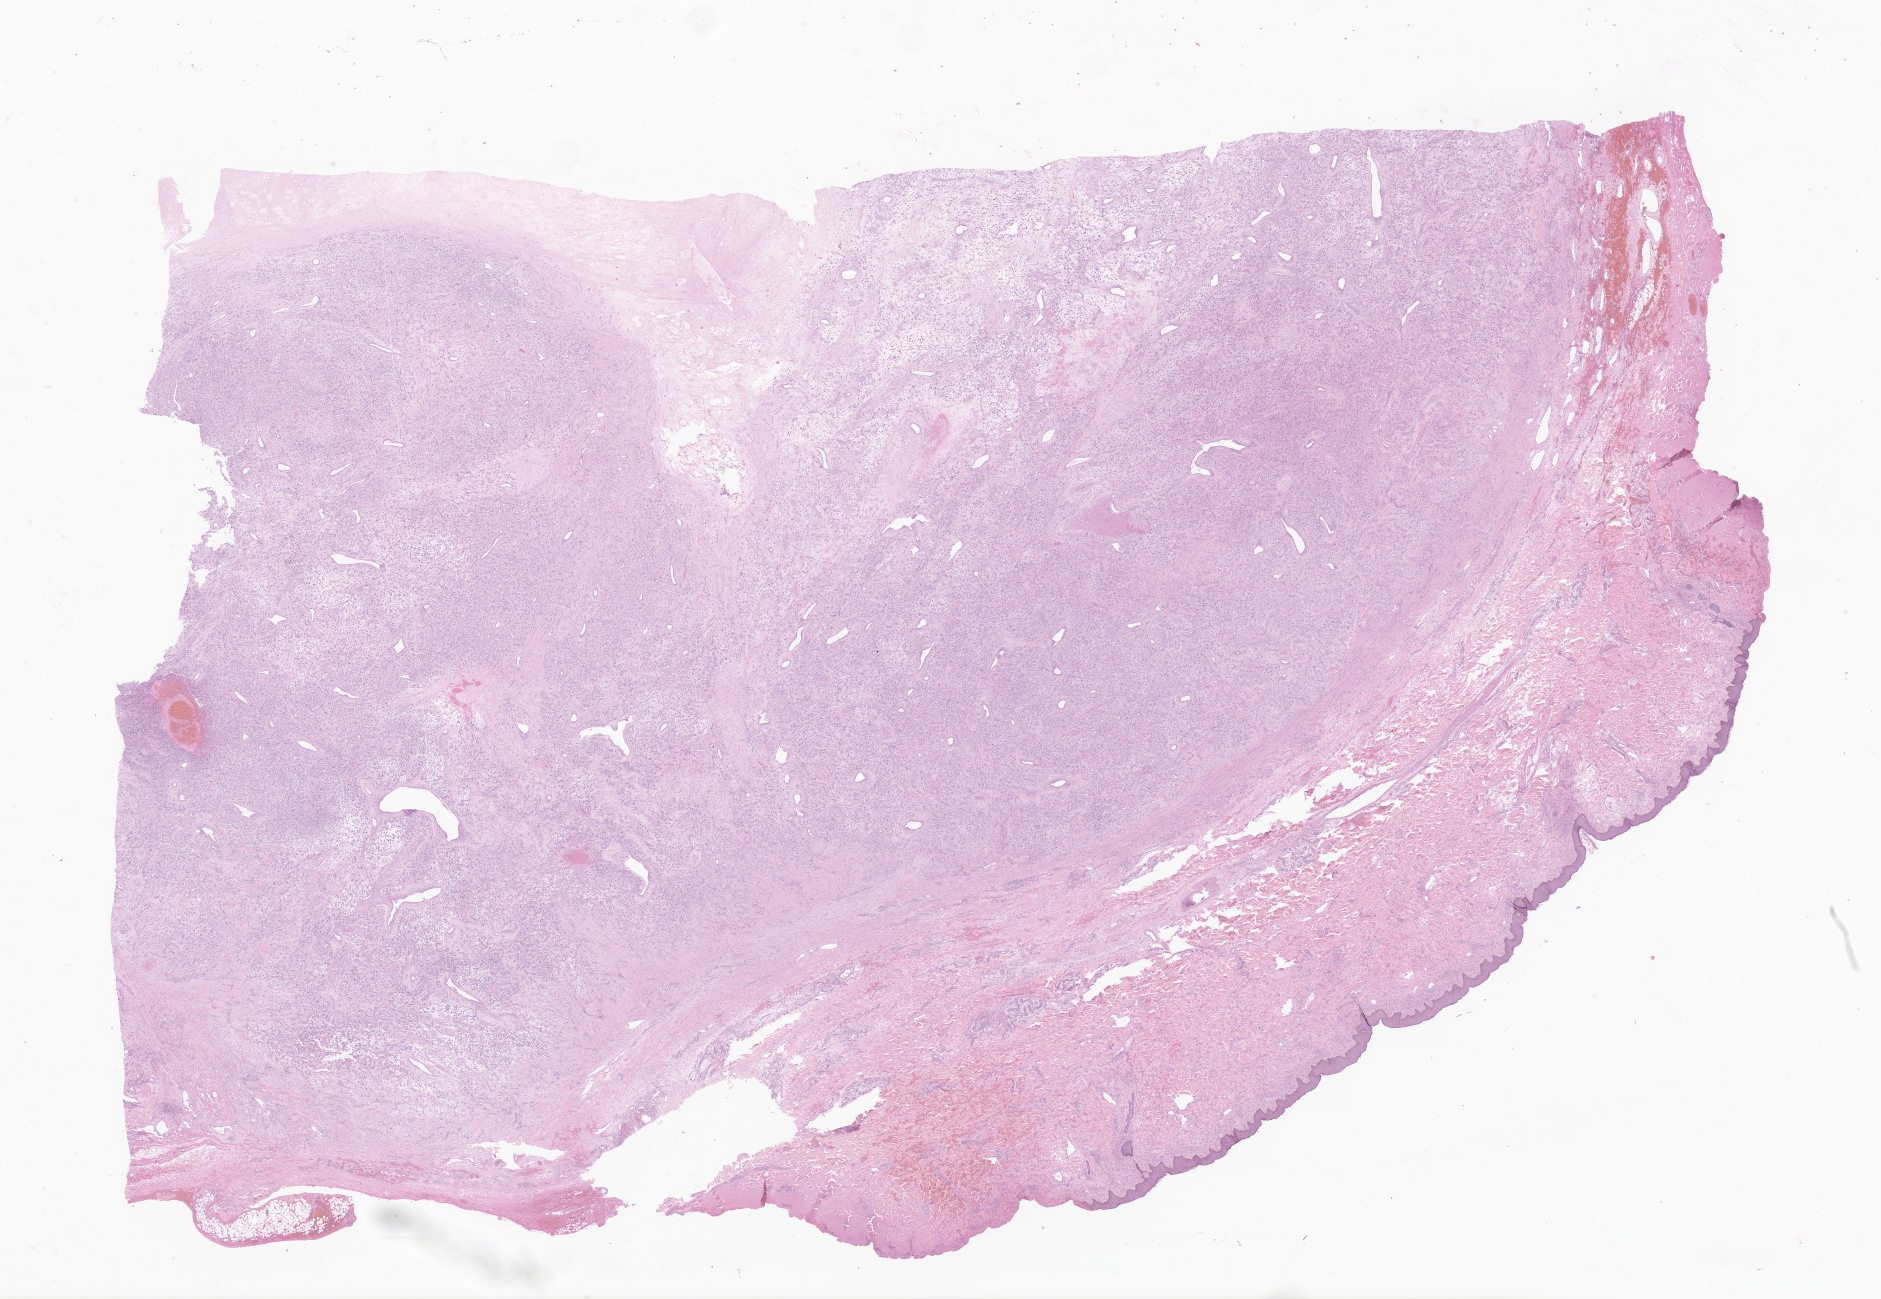
Whole-slide image, haematoxylin and eosin stain of tumor tissue from the thorax — shown as a low-resolution overview of the whole scanned area (about 31.7 x 21.9 mm), FFPE section. Male patient, age 174 months (14 years 6 months).
Diagnosis: Malignant peripheral nerve sheath tumor, NOS.